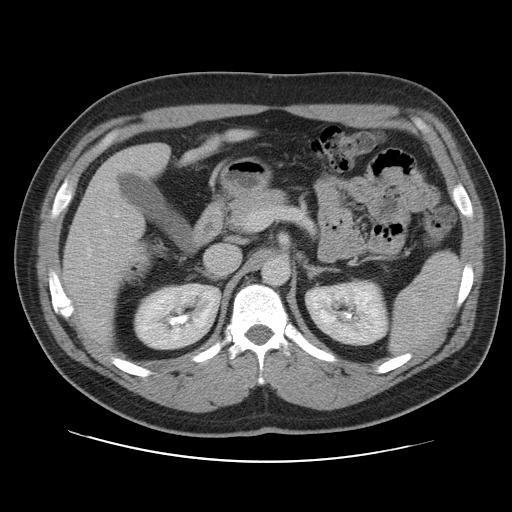
Contrast-enhanced abdominal CT, one axial slice. Slice 62 of 109 in the series (ordered by position). 120 kVp. Soft-tissue window (W 400 / L 40 HU). 512 × 512 image matrix, field of view 402 × 402 mm. Male patient, age 35 years. From the clinical record (not read from this slice): diagnosis: colorectal cancer liver metastases, imaged before liver resection; multiple liver metastases: yes; largest metastasis: 2.8 cm; disease in both lobes: yes.
Annotated regions visible in this slice (expert manual segmentation):
- liver: box from (x=64, y=144) to (x=169, y=346) px
- planned liver remnant (the part of the liver to remain after resection): (x=64, y=140)–(x=217, y=346)
- portal vein (with intrahepatic branches): (x=90, y=208)–(x=120, y=285)